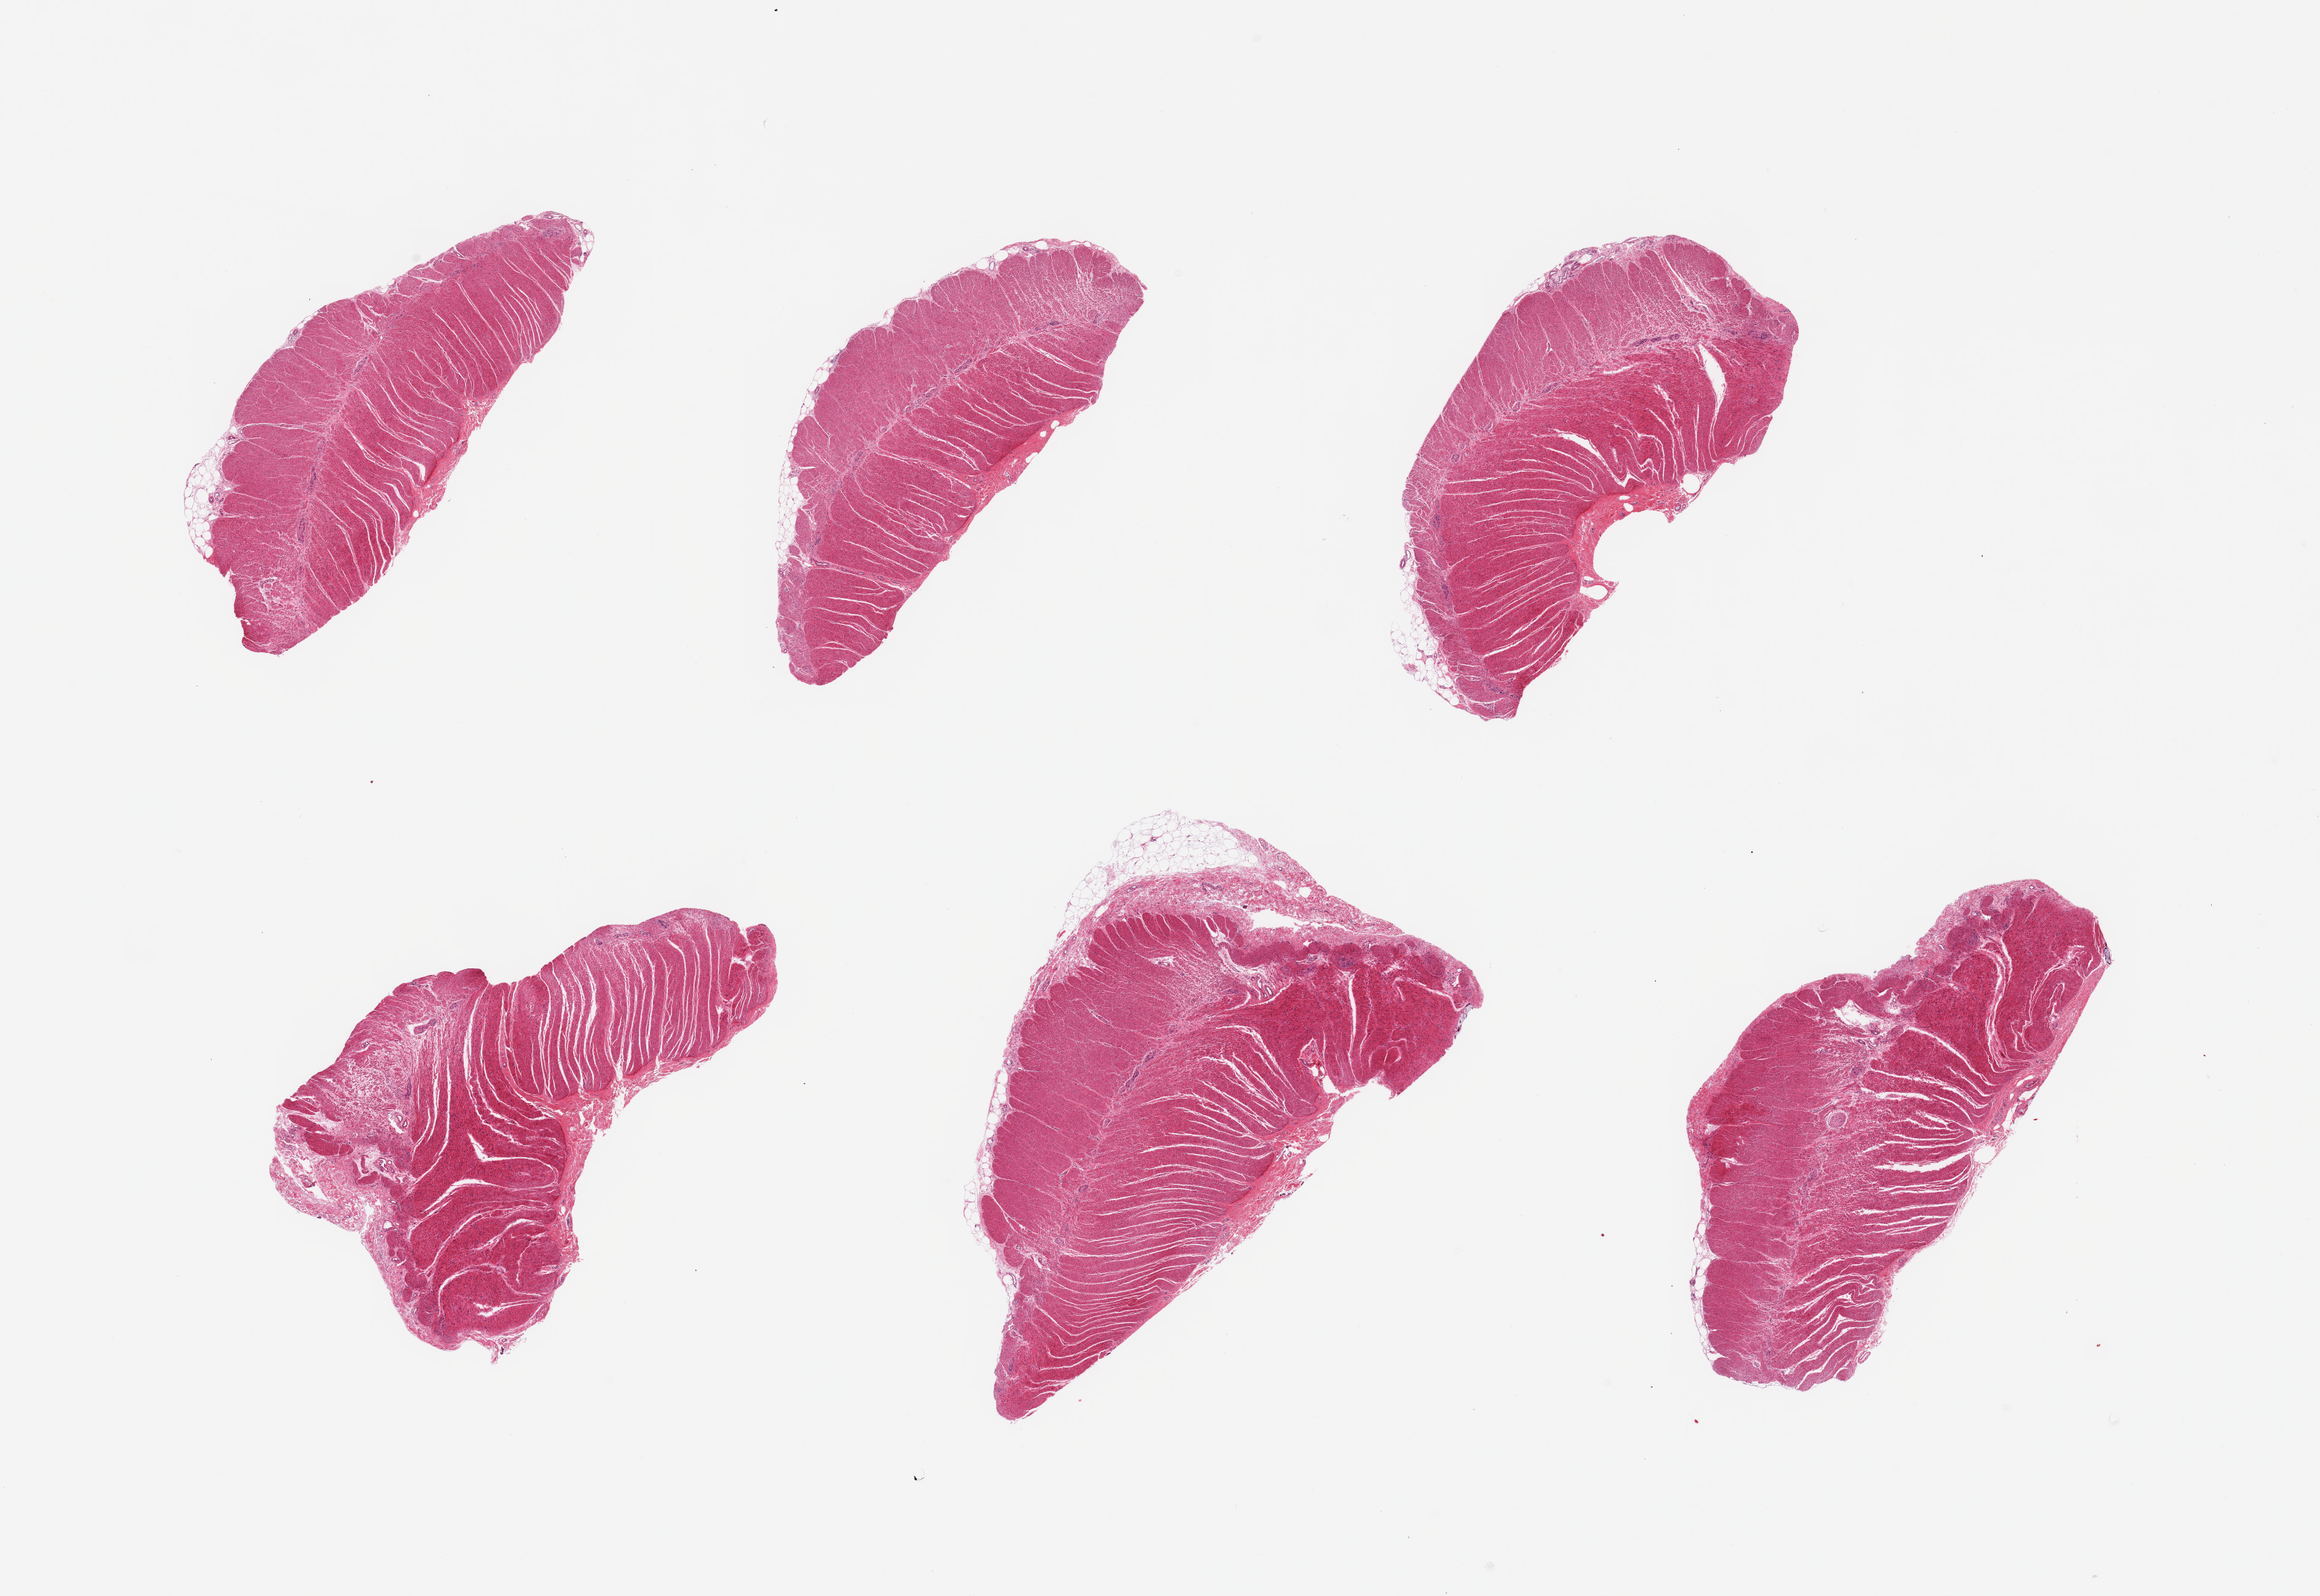
Digitized H&E-stained section — shown as a low-resolution overview of the whole scanned area (about 24.6 x 16.9 mm). PAXgene-fixed, paraffin-embedded tissue. Sampled site (target tissue): sigmoid colon. Tissue donor sample. Male donor.
Review note (as recorded): 6 pieces; well trimmed target muscularis.